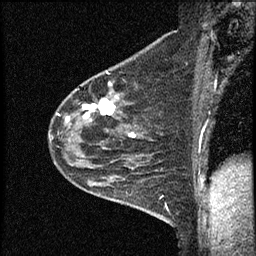
Breast MRI (dynamic contrast-enhanced), one sagittal slice. Position 44 of 60 along the scan axis. Dynamic contrast-enhanced study with each time point stored as its own series, time point 2 of 4 at this slice position (early post-contrast, ordered by acquisition time). 1.5 T. TE 4.2 ms, TR 17.6 ms. 256 × 256 image matrix, field of view 200 × 200 mm. Female patient, age 53 years. From the clinical record (not read from this slice): setting: breast cancer imaged before/during neoadjuvant chemotherapy; receptor status: HR-positive, HER2-negative.
Structures marked on this image (semi-automatically segmented with operator editing):
- analysis volume of interest (the breast-tissue region the enhancement analysis was run in; not a lesion): bounding box [x1, y1, x2, y2] px = [48, 69, 156, 199]
- tumour enhancement mask (voxels above the 100 % enhancement threshold inside the analysis volume of interest): [66, 83, 135, 137]